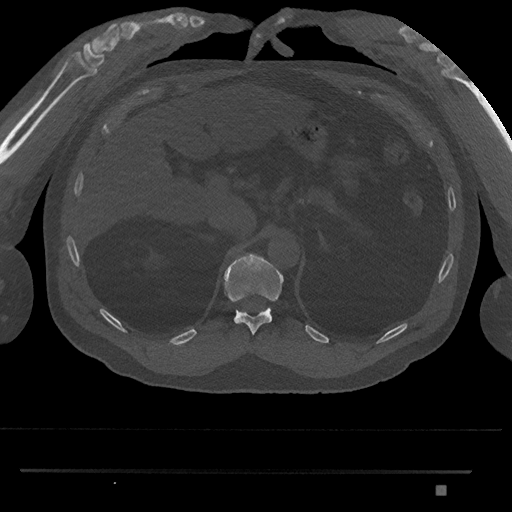
CT including the spine, one axial slice; slice 938 of 1134 in the series (ordered by position); reconstruction kernel Br40s/3; 120 kVp; bone window (W 1800 / L 400 HU); 512 × 512 image matrix, field of view 429 × 429 mm. Male patient, age 65 years. Case-level facts recorded for this patient, not image findings: primary cancer: prostate.
Outlined on this slice (semi-automatically segmented with operator editing):
- T11 vertebra: bounding box (x1, y1, x2, y2) in pixels: (223, 254, 284, 335)